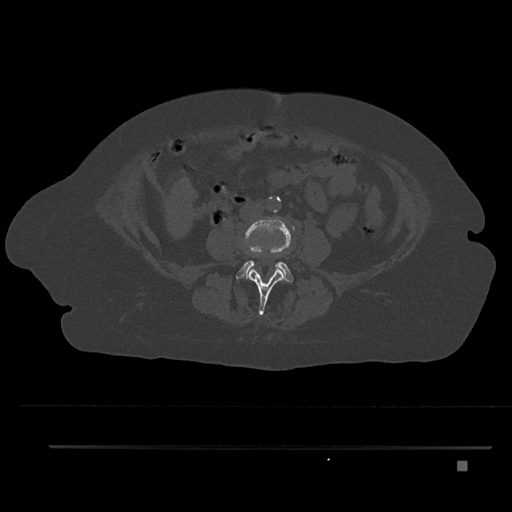
CT including the spine, one axial slice; reconstruction kernel Br40s/3; bone window (W 1800 / L 400 HU); 512 × 512 image matrix. Female patient, age 76 years. Case-level facts recorded for this patient, not image findings: primary cancer: lung; vertebrae with lytic lesions (as recorded): T11, L3.
Outlined on this slice (semi-automatic segmentation, software-assisted and operator-edited):
- L3 vertebra: box from (x=249, y=266) to (x=285, y=315) px
- L4 vertebra: (x=236, y=218)–(x=293, y=283)